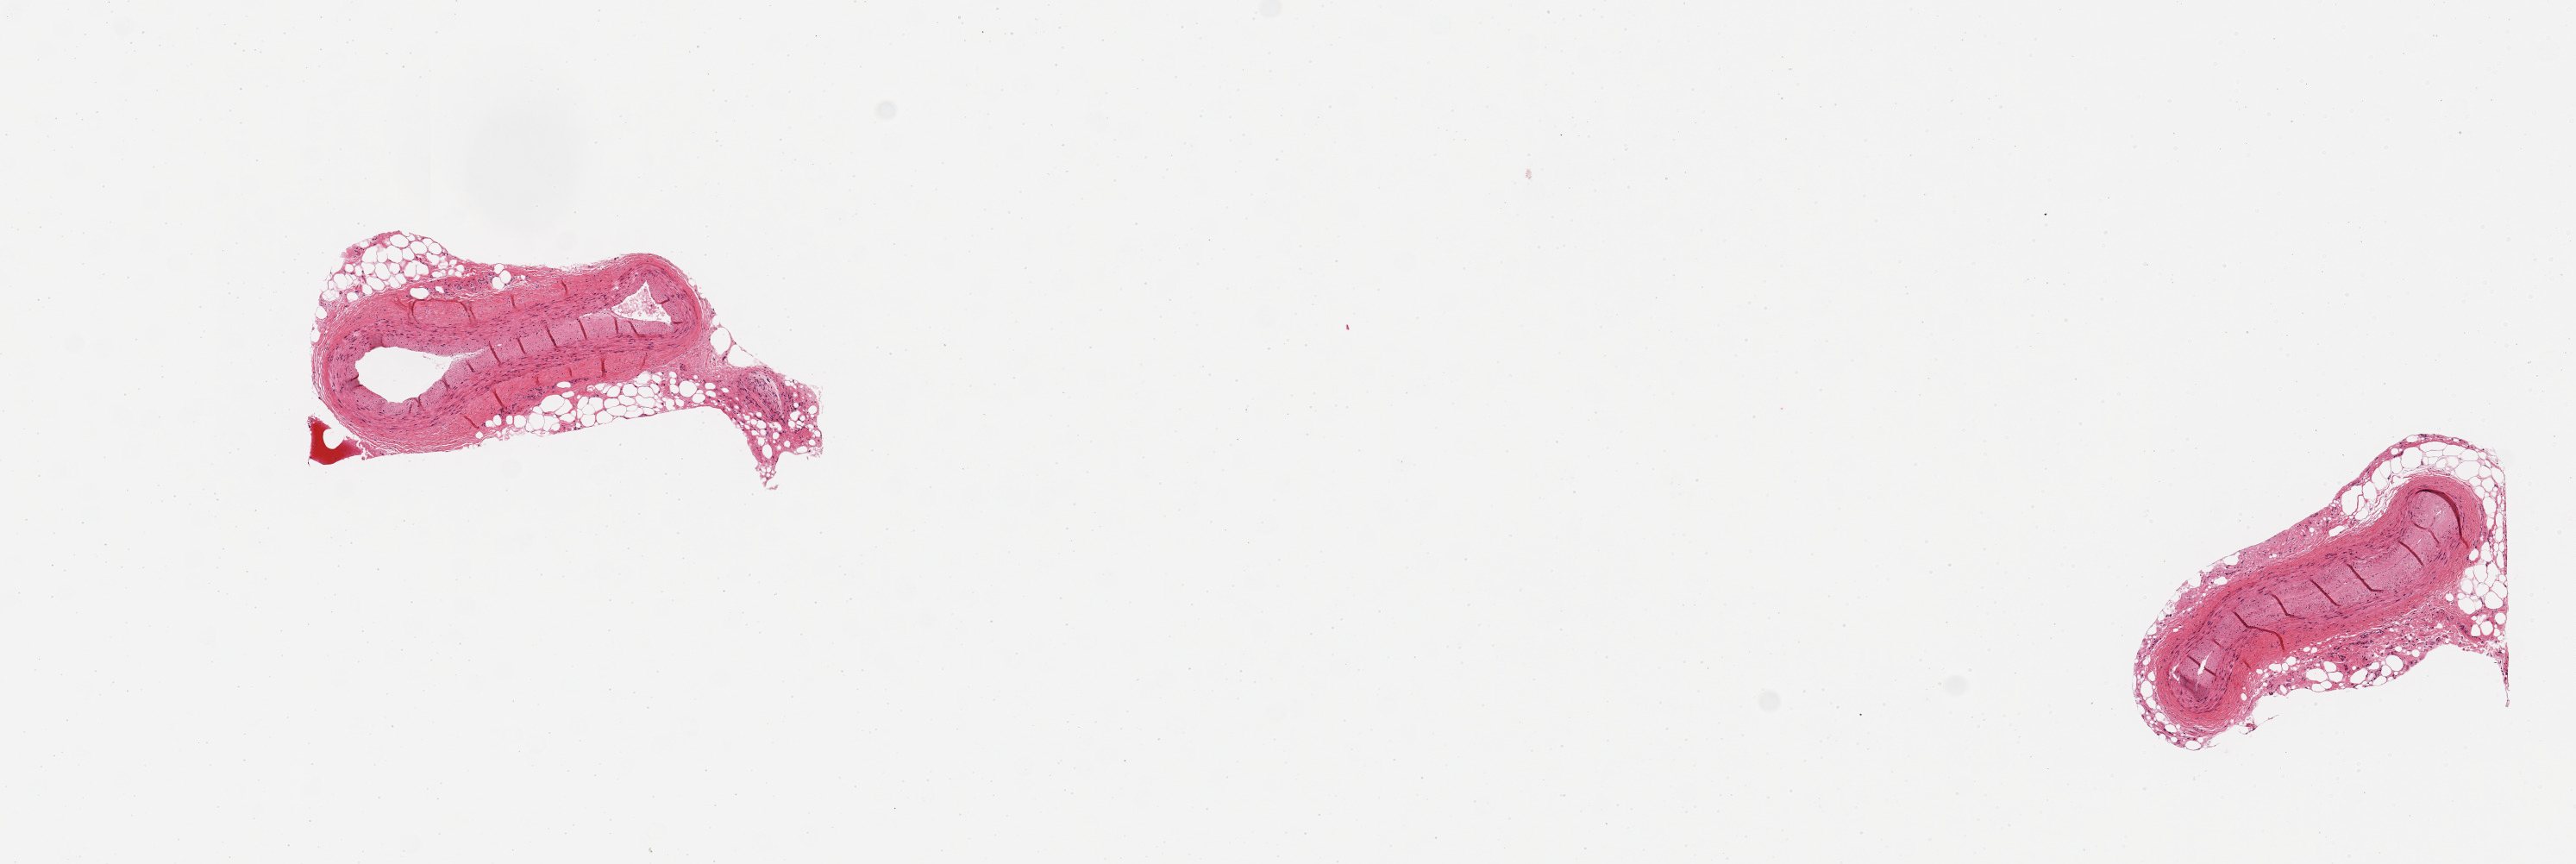
Hematoxylin and eosin (H&E) whole-slide image, brightfield, low-resolution overview of the scanned area, about 11.8 x 4.0 mm. PAXgene-fixed, paraffin-embedded tissue. Target tissue: coronary artery. Donor tissue sample. Donor sex: male.
Reviewer comment on this tissue sample: 2 pieces; rim of adipose tissue and nerve, from 30-50% of the specimen, mild atherosclerosis.